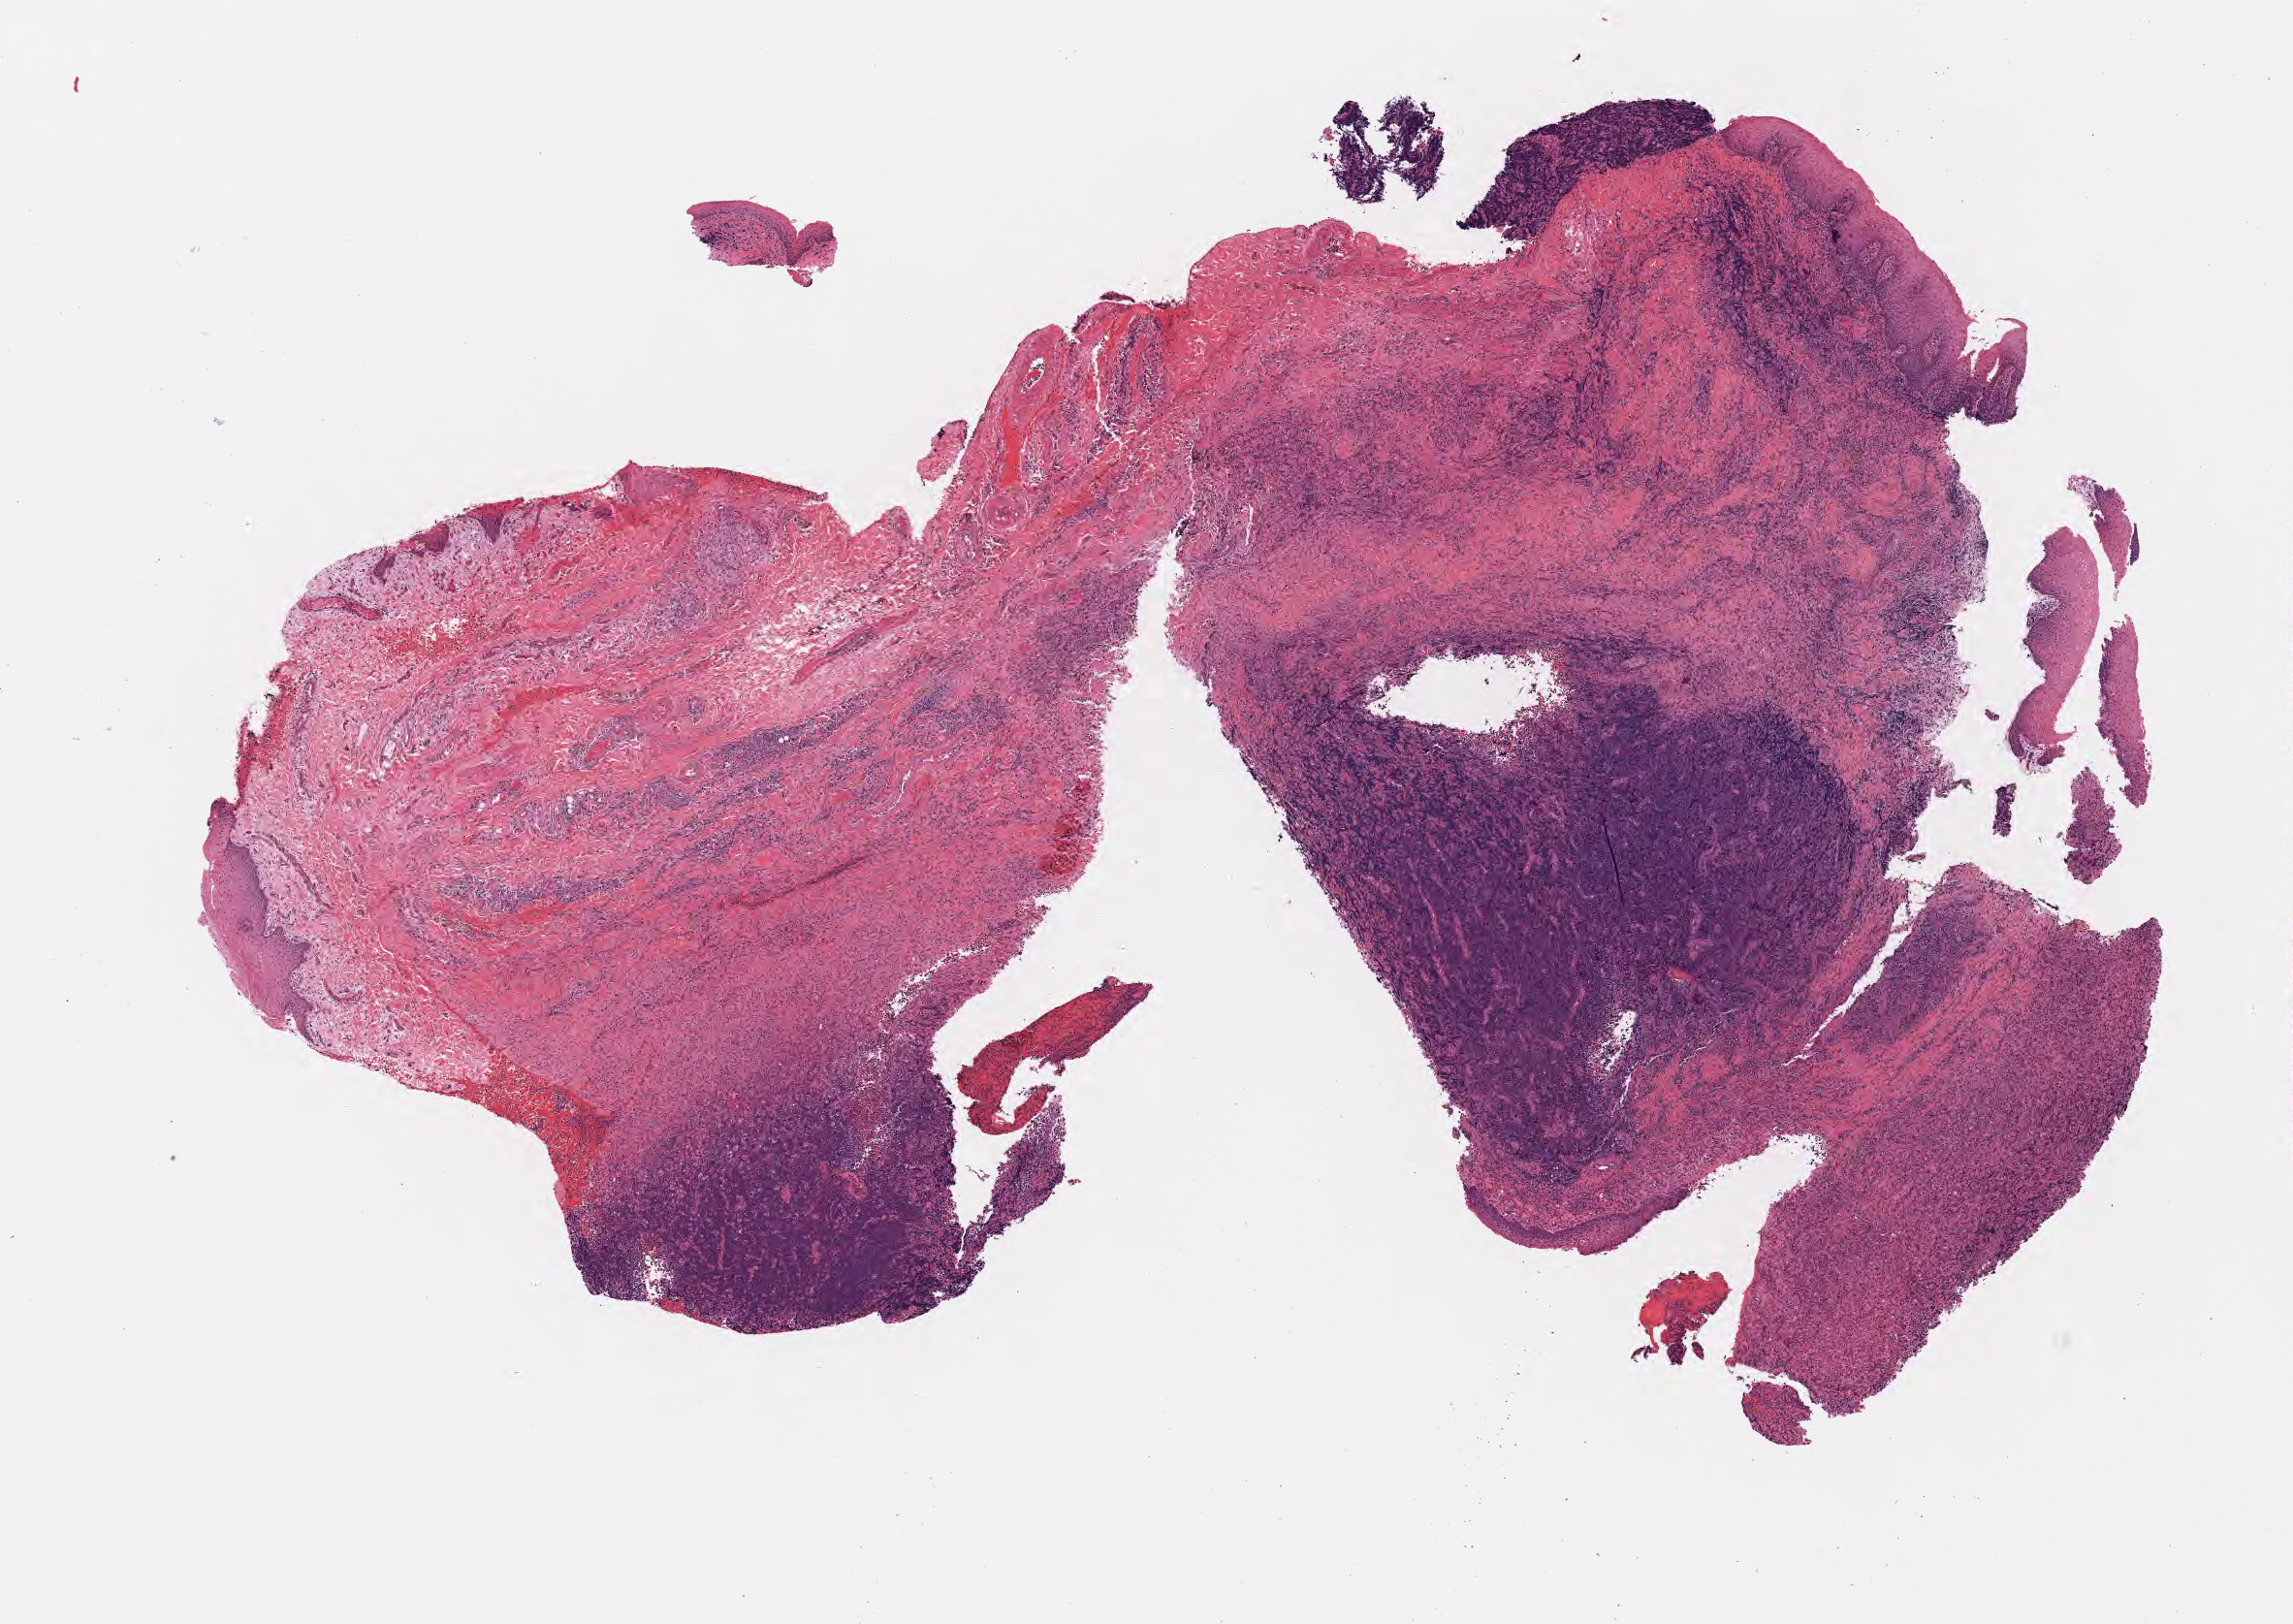
Whole-slide image, haematoxylin and eosin stain, low-resolution overview of the scanned area, about 9.6 x 6.8 mm; specimen: tumor tissue; anatomic site: cranium. Patient: male, 10 years old.
* diagnosis: Burkitt lymphoma, NOS